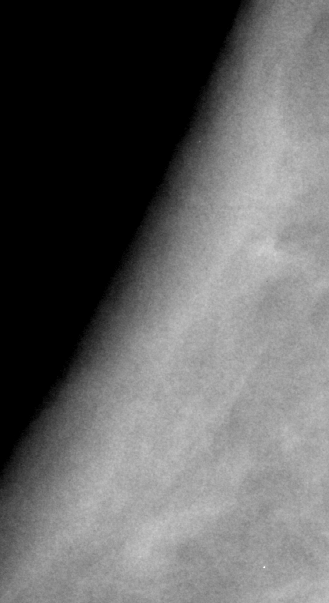
Cropped region of a digitized screen-film mammogram centred on a radiologist-marked abnormality, right breast, CC view, BI-RADS breast density category 2 (scale 1–4).
- Mass, shape irregular / architectural distortion, margins ill defined / spiculated; BI-RADS assessment category 5; subtlety rating 5 on a 1 (subtle) to 5 (obvious) scale; pathology result (as recorded, not read from the image): malignant.